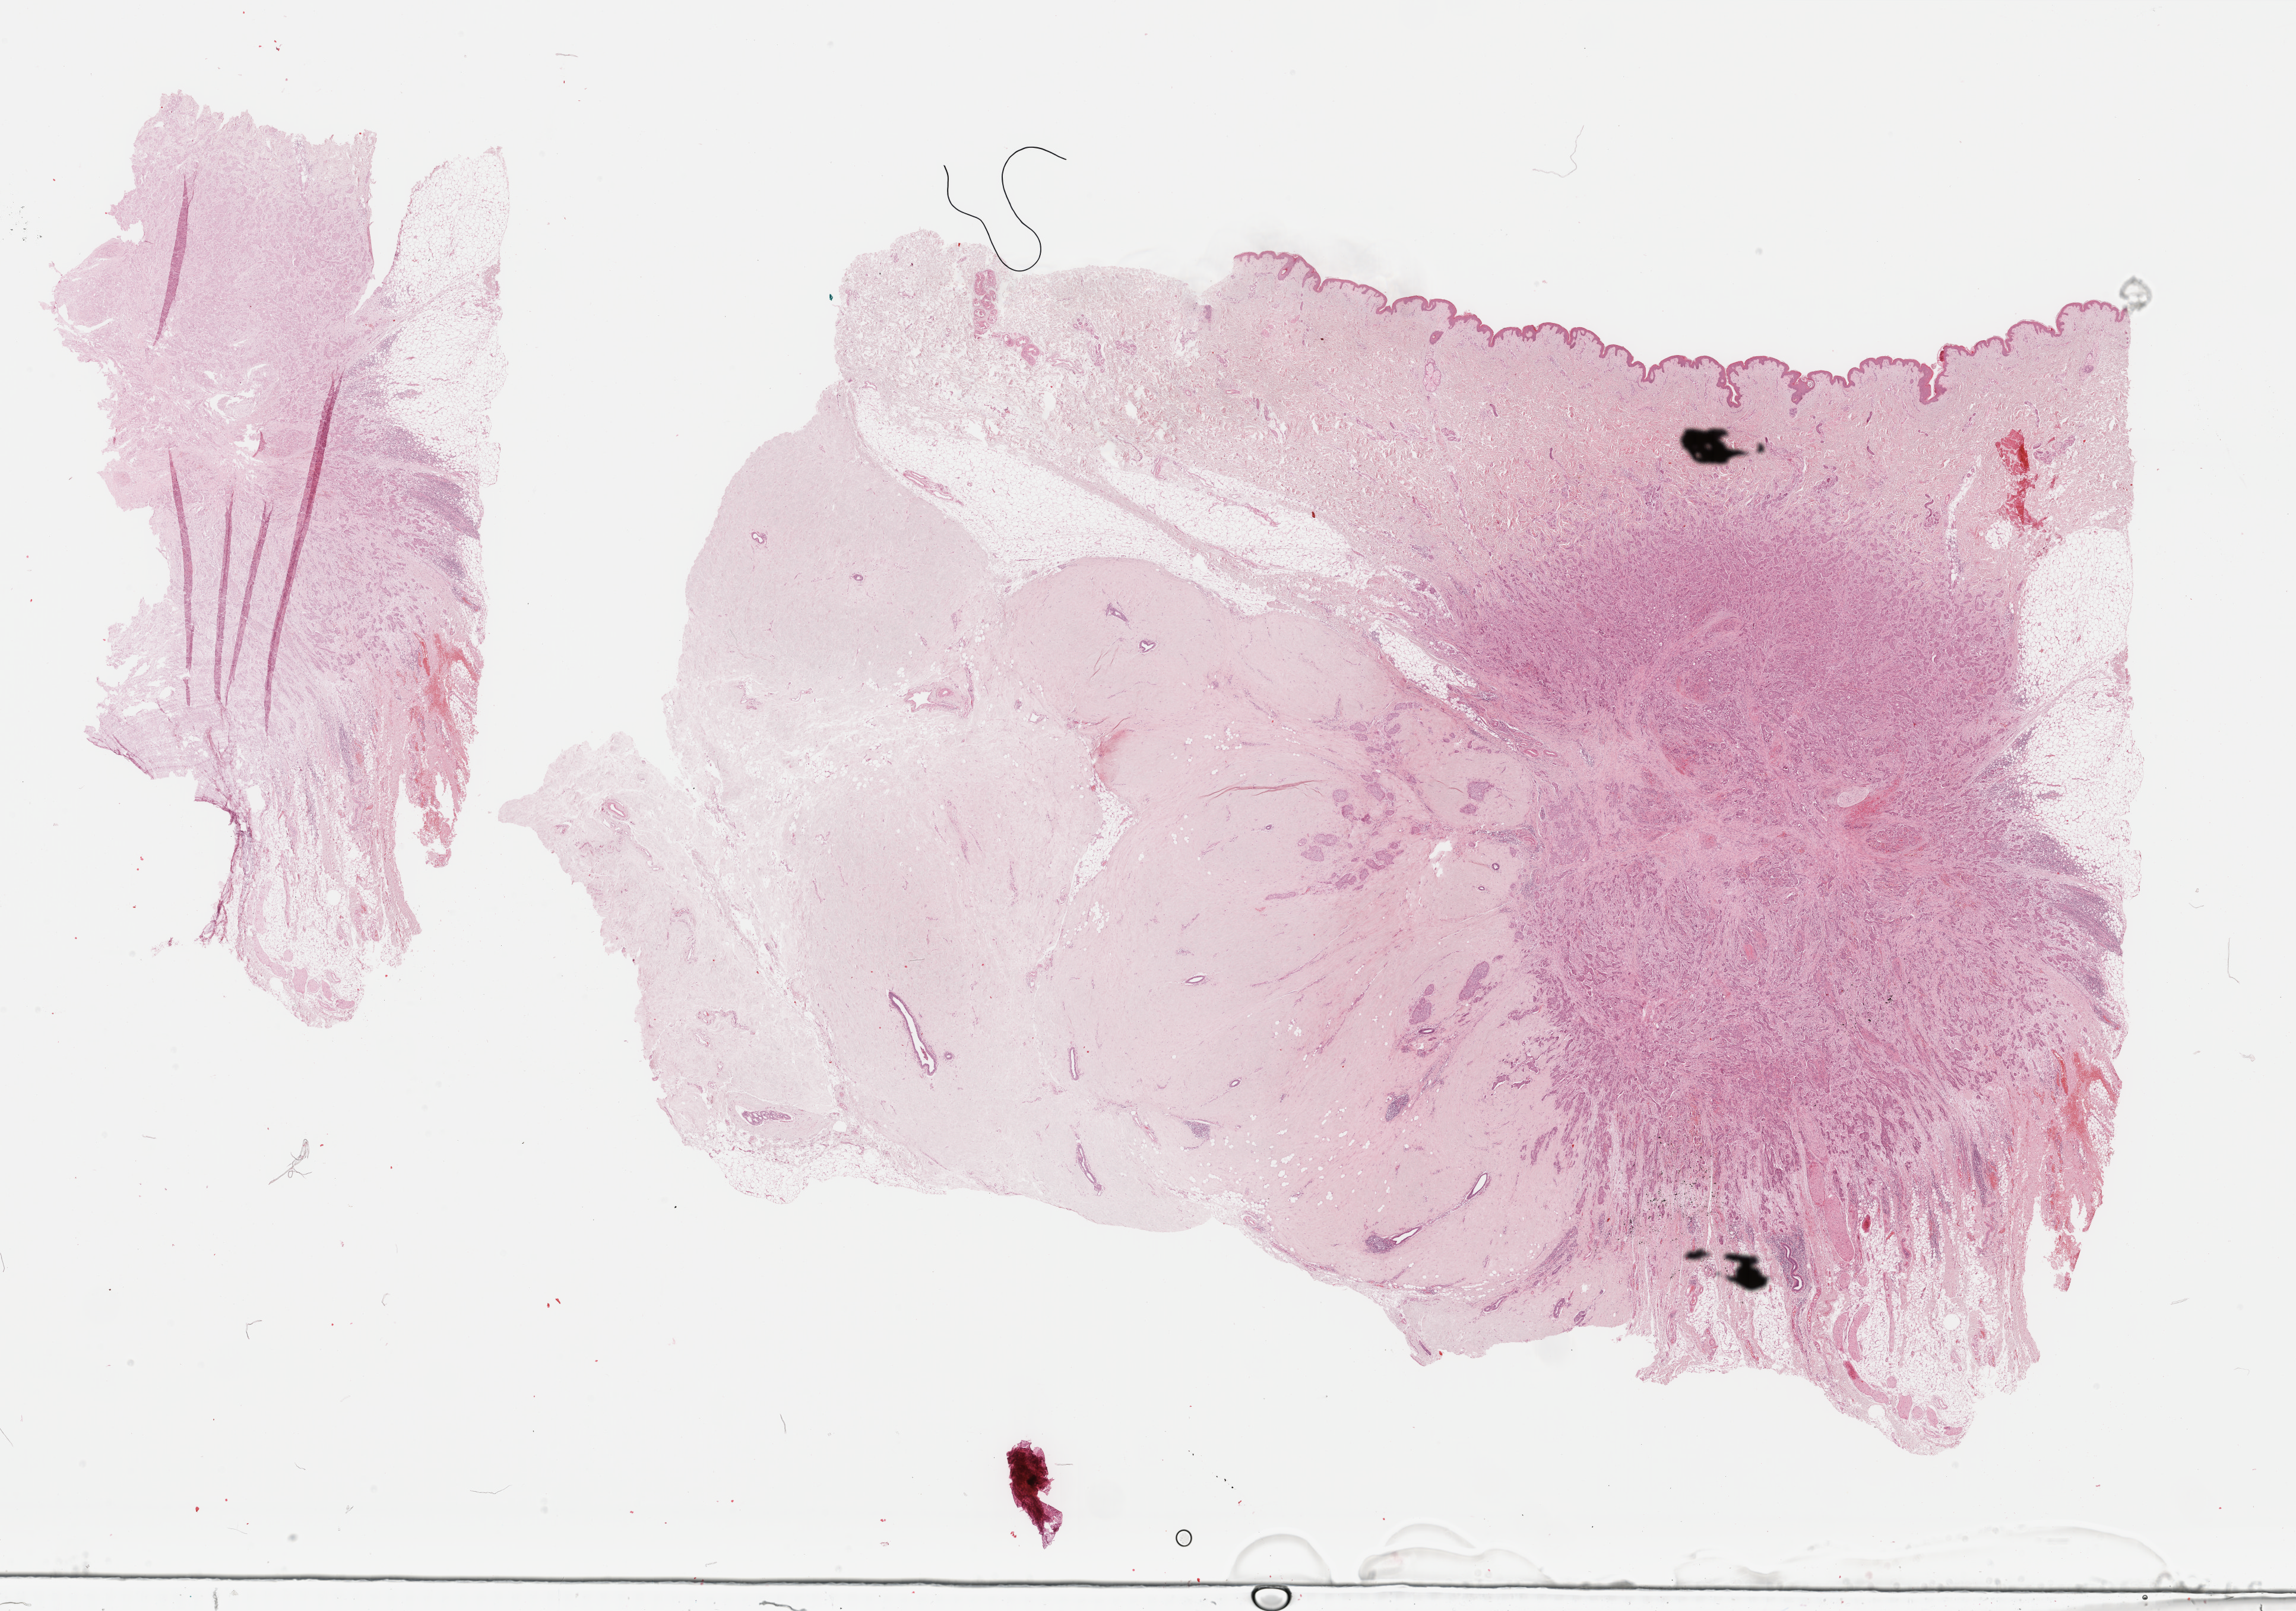
Hematoxylin and eosin (H&E) stained whole-slide image, whole scanned area (about 30.7 x 21.5 mm, from a 40x scan) shown as a low-resolution overview, formalin-fixed paraffin-embedded (FFPE) diagnostic section, breast, primary tumour sample. Female patient; age at initial diagnosis 56 years.
Histologic diagnosis: Infiltrating duct carcinoma, NOS.